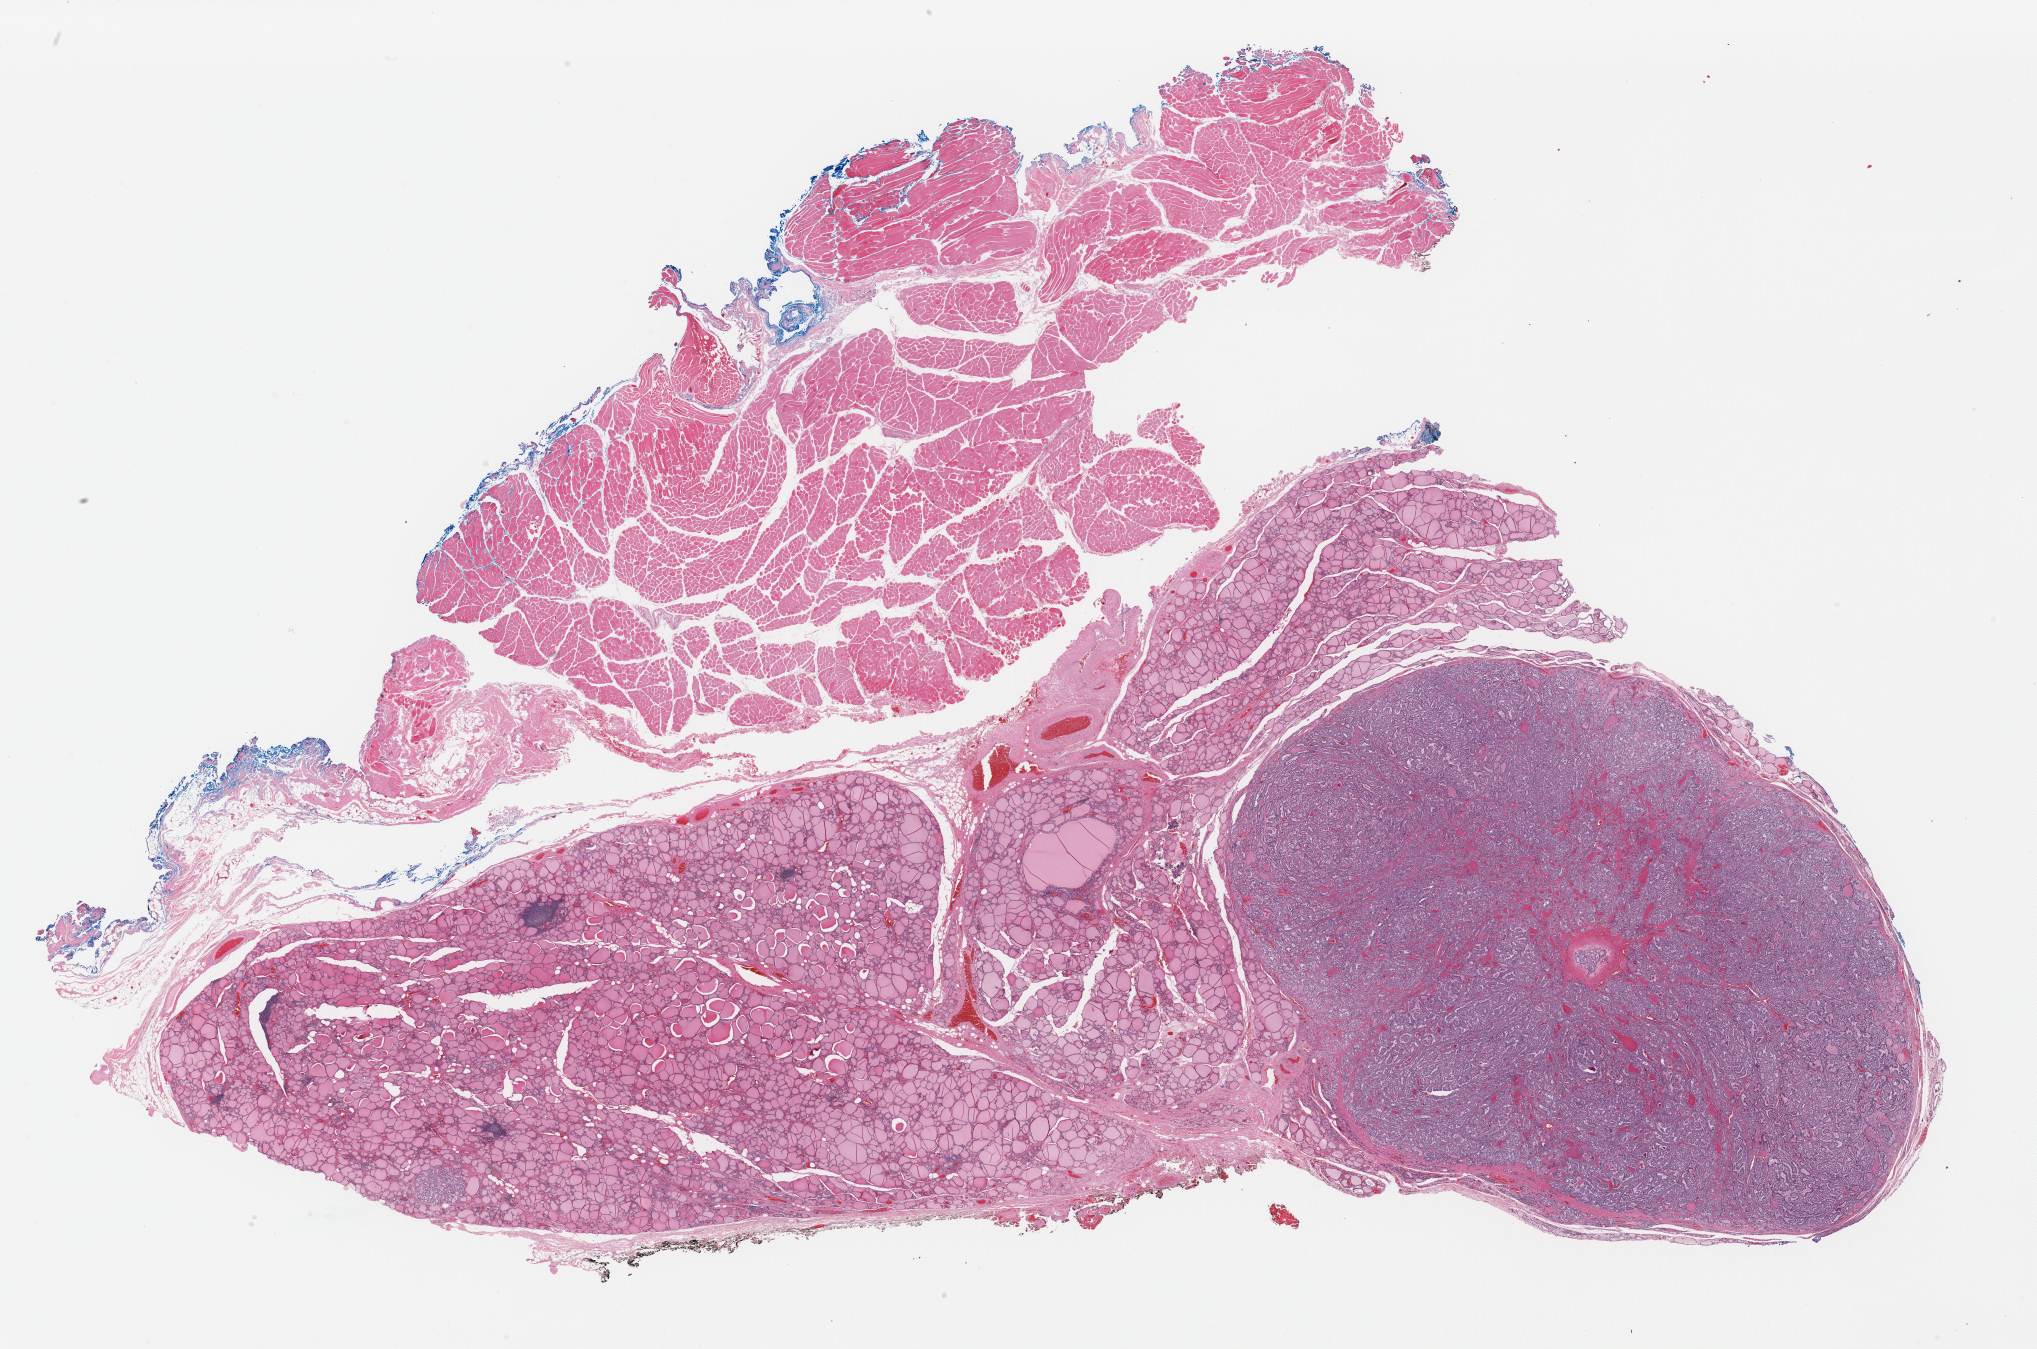
Whole-slide histology image, H&E — whole scanned area (about 32.1 x 21.3 mm, acquisition: 40x scan) shown as a low-resolution overview; FFPE section; thyroid, primary tumour sample. Patient: female, age at initial diagnosis 51 years.
Laterality: left. Diagnosis: Papillary adenocarcinoma, NOS. AJCC pathologic stage: I (7th edition). Lymph nodes positive (case pathology): 0 of 3 examined.